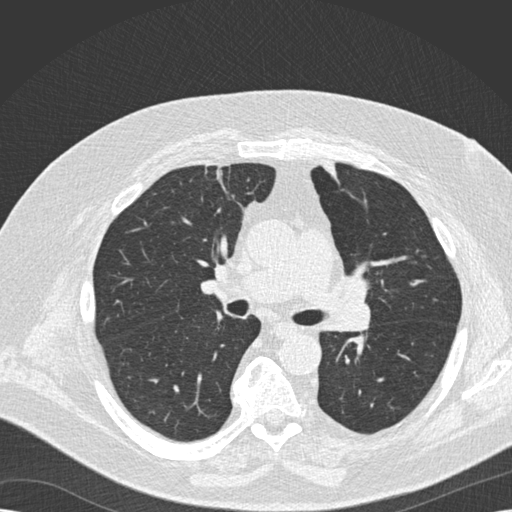
Low-dose screening chest CT, one axial slice. Slice 101 of 173 in the series (ordered by position). Reconstruction kernel B30f. Lung window (W 1500 / L -600 HU). 512 × 512 image matrix, field of view 370 × 370 mm.
Structures marked on this image (expert manual segmentation):
- lesion 1 (tumor, upper lobe of left lung): box from (x=321, y=158) to (x=339, y=178) px